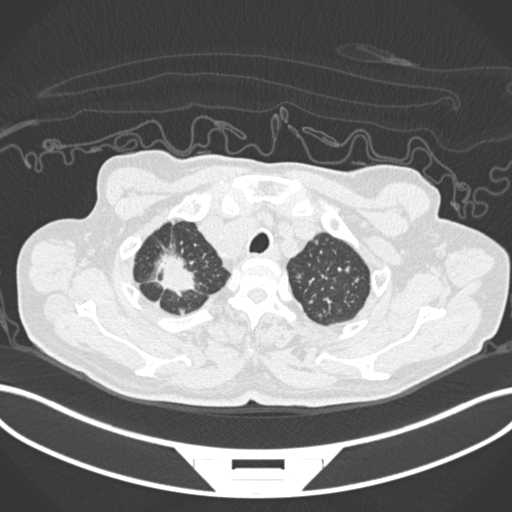
Chest CT, one axial slice; slice 194 of 207 in the series (ordered by position); reconstruction kernel B30f; 120 kVp; lung window (W 1500 / L -600 HU); 512 × 512 image matrix, field of view 400 × 400 mm. Male patient, age 69 years. From the clinical record (not read from this slice): clinical TNM (as recorded): T1c N1 M1.
Outlined on this slice (rectangle marked by the reading radiologist):
- lung tumour (recorded histology: adenocarcinoma): box from (x=151, y=246) to (x=200, y=296) px